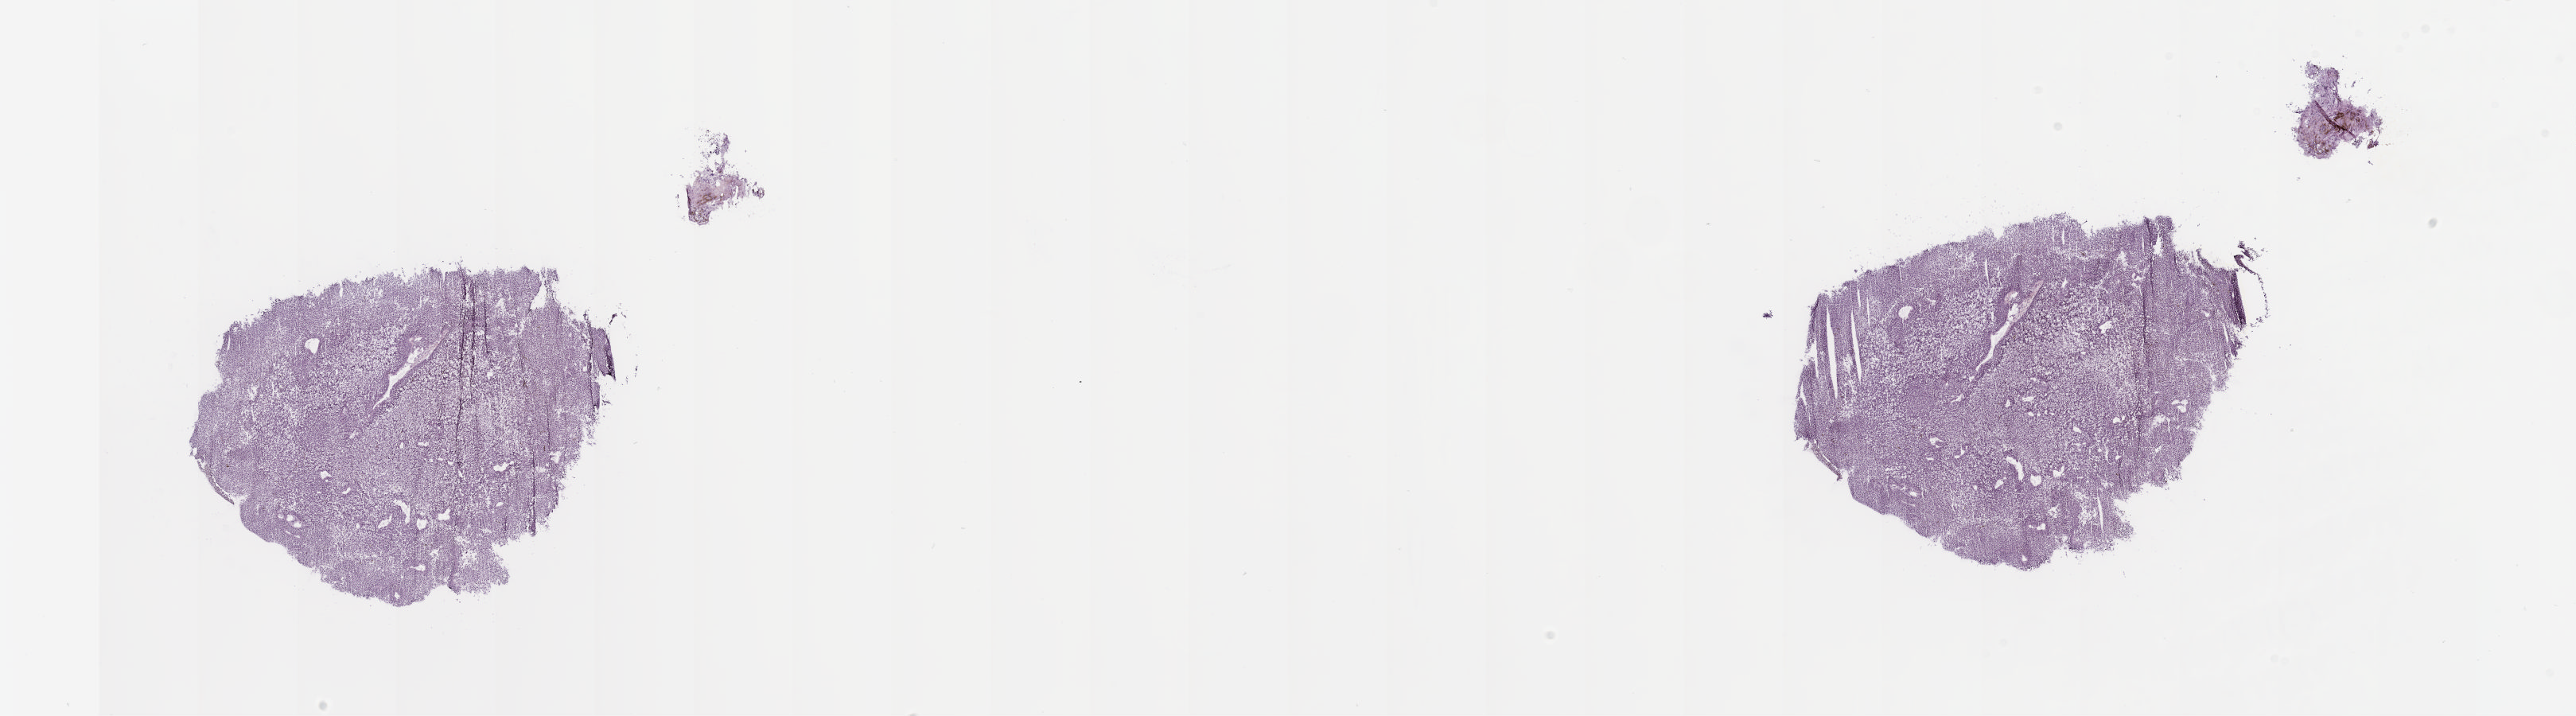
Whole-slide histology image, Hematoxylin and eosin (H&E) stained — whole scanned area (about 26.1 x 7.2 mm, acquisition: 20x scan) shown as a low-resolution overview. Frozen section. Sample: primary tumour, uvea. Patient: female, age at initial diagnosis 75 years. Composition of this section per pathologist review: tumour cells 90%, tumour nuclei 95%, normal cells 0%, stromal cells 10%, necrosis 0%. Inflammatory infiltration, as recorded: lymphocyte infiltration 0%, monocyte infiltration 0%, neutrophil infiltration 0%.
AJCC pathologic stage: IIB (7th edition). Diagnosis: Spindle cell melanoma, NOS.